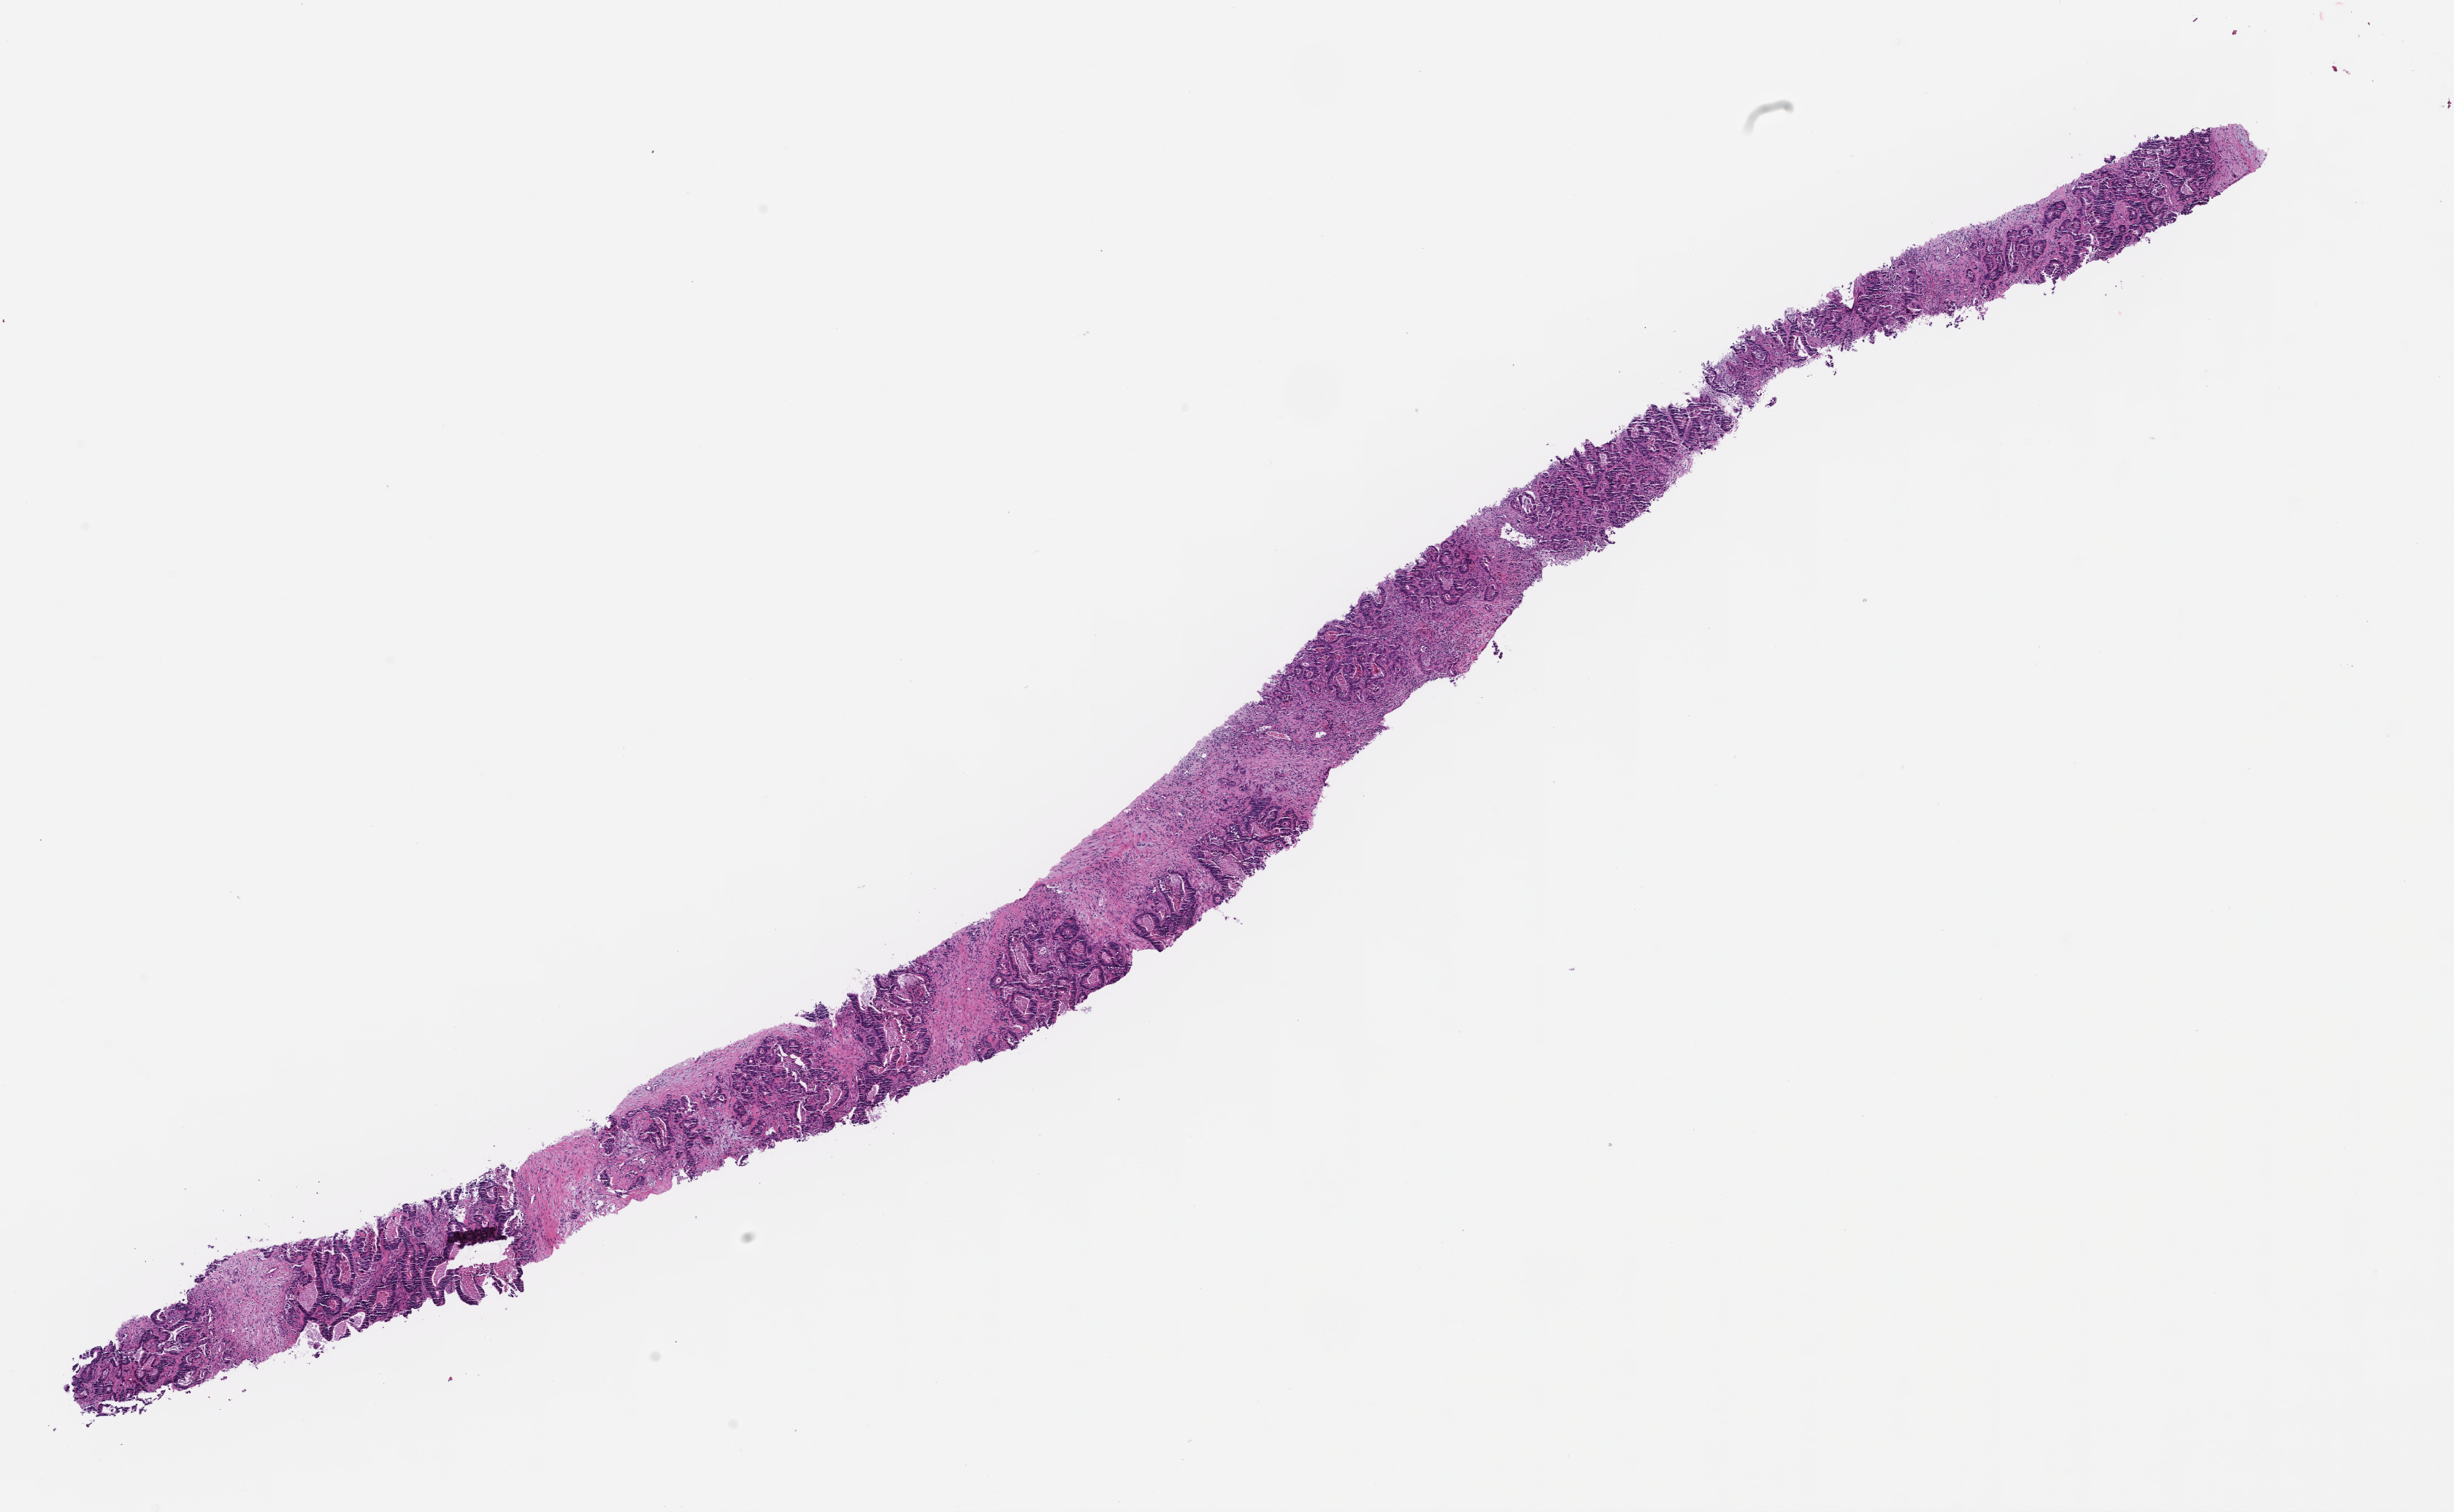
Haematoxylin and eosin whole-slide image, whole scanned area (about 13.6 x 8.4 mm) shown as a low-resolution overview. Formalin-fixed paraffin-embedded section. Tissue site: colon. Specimen time point: collected at baseline (before treatment). Patient: male.
This section: primary tumor. Diagnosis: Colorectal Carcinoma.